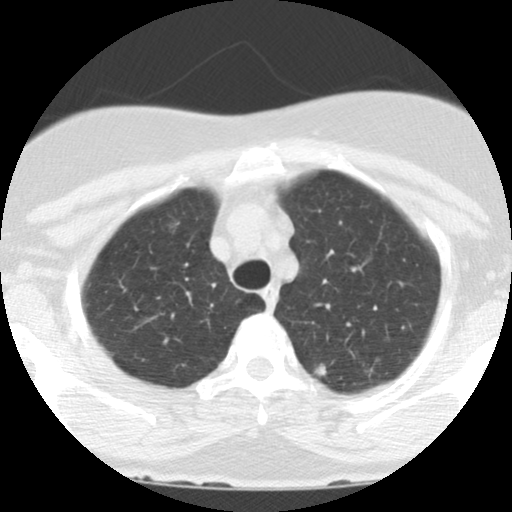
Low-dose screening chest CT, axial slice. Baseline annual screen. Lung window (W 1500 / L -600 HU). 2.5 mm slice thickness. Female participant, aged 60 years at enrolment.
Expert-annotated lung lesion, bounding box (x1, y1, x2, y2) in pixels: (304, 355, 338, 385). The screening reader recorded 3 non-calcified nodules or masses ≥4 mm on this exam; which of them this box marks is not recorded. Later outcome: lung cancer diagnosed 31 days after this screen — bronchiolo-alveolar adenocarcinoma, NOS, left upper lobe, moderately differentiated (G2), stage IA (AJCC 6th edition), 15 mm at pathology.